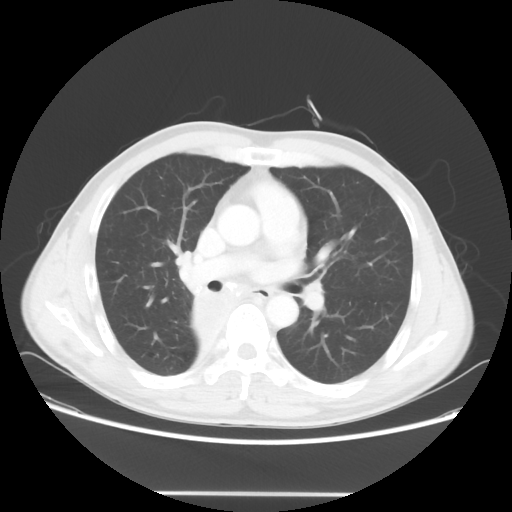
Chest CT, one axial slice. Reconstruction kernel STANDARD. Lung window (W 1500 / L -600 HU). 5 mm slice thickness. 512 × 512 image matrix, field of view 393 × 393 mm. Patient: male, 47 years. Case-level facts recorded for this patient, not image findings: clinical TNM (as recorded): T2 N0 M0; histopathological grade: G2.
Structures marked on this image (rectangle marked by the reading radiologist):
- lung tumour (recorded histology: squamous cell carcinoma): bounding box (x1, y1, x2, y2) in pixels: (181, 286, 239, 346)